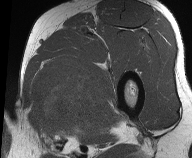
MRI of an extremity soft-tissue mass, one axial slice; position 39 of 61 along the scan axis; MR volume resampled by the dataset authors to the PET/CT grid (not the native acquisition matrix); 3.27 mm slice thickness; 192 × 158 image matrix. Male patient. Case-level facts recorded for this patient, not image findings: histological type: pleiomorphic liposarcoma; grade: high; site of the primary tumour: left thigh.
Annotated regions visible in this slice (expert contour drawn on MRI and transferred to this co-registered scan by the dataset authors):
- gross tumour volume including surrounding oedema: box from (x=29, y=55) to (x=104, y=141) px
- gross tumour volume (mass): (x=32, y=60)–(x=99, y=125)